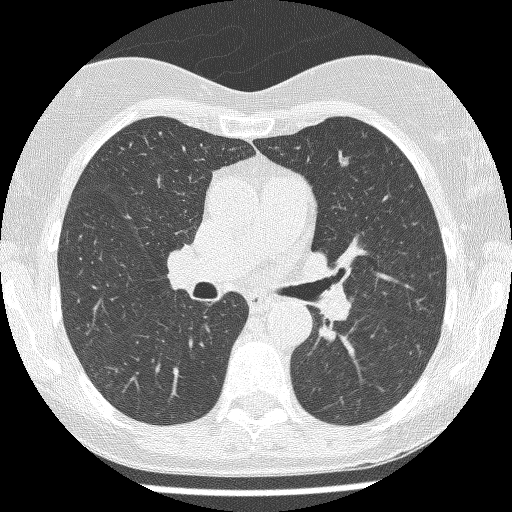
Low-dose screening chest CT, axial slice, baseline screening round, lung window (W 1500 / L -600 HU), 1.25 mm slice thickness, lung (sharp) reconstruction kernel (BONE), slice 147 of 237 in the series, 512 × 512 image matrix. Female, age 60 years at enrolment. Current smoker at enrolment.
Lesion marked by an expert reader, bounding box (x1, y1, x2, y2) in pixels: (332, 151, 359, 174). Reader record for this screening exam (exam-level; its link to the box is not recorded): non-calcified nodule or mass ≥4 mm, lingula, 5 × 4 mm, smooth margins, soft tissue attenuation.